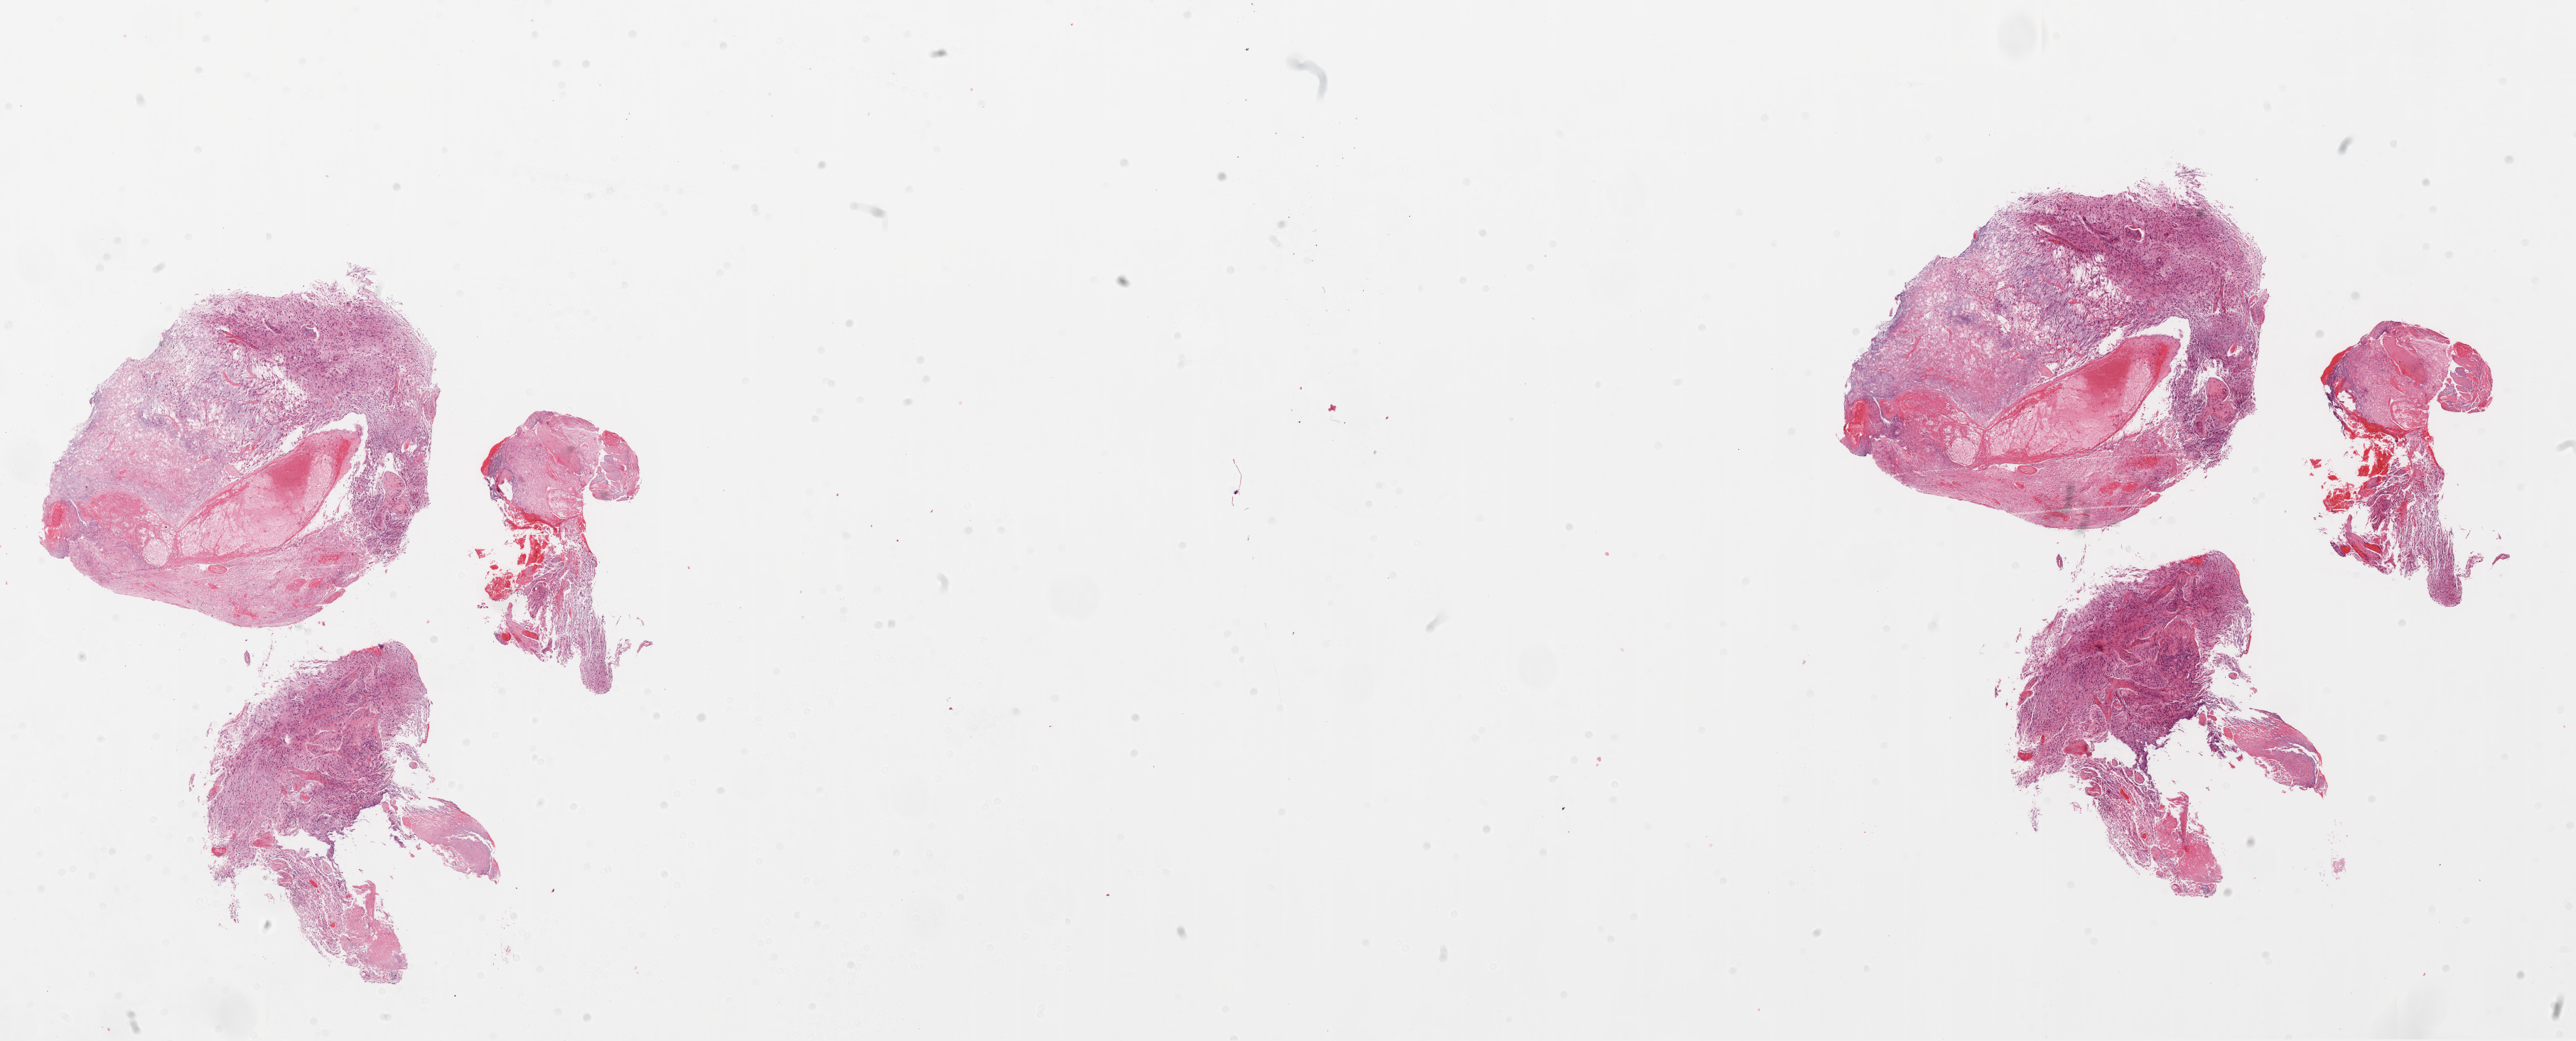
Digitized H&E tissue section (whole slide), shown as a low-resolution overview of the whole scanned area (about 29.1 x 11.8 mm); FFPE section; sample: primary tumour, brain. Male patient; age at initial diagnosis 79 years.
Pathologic diagnosis: Glioblastoma.